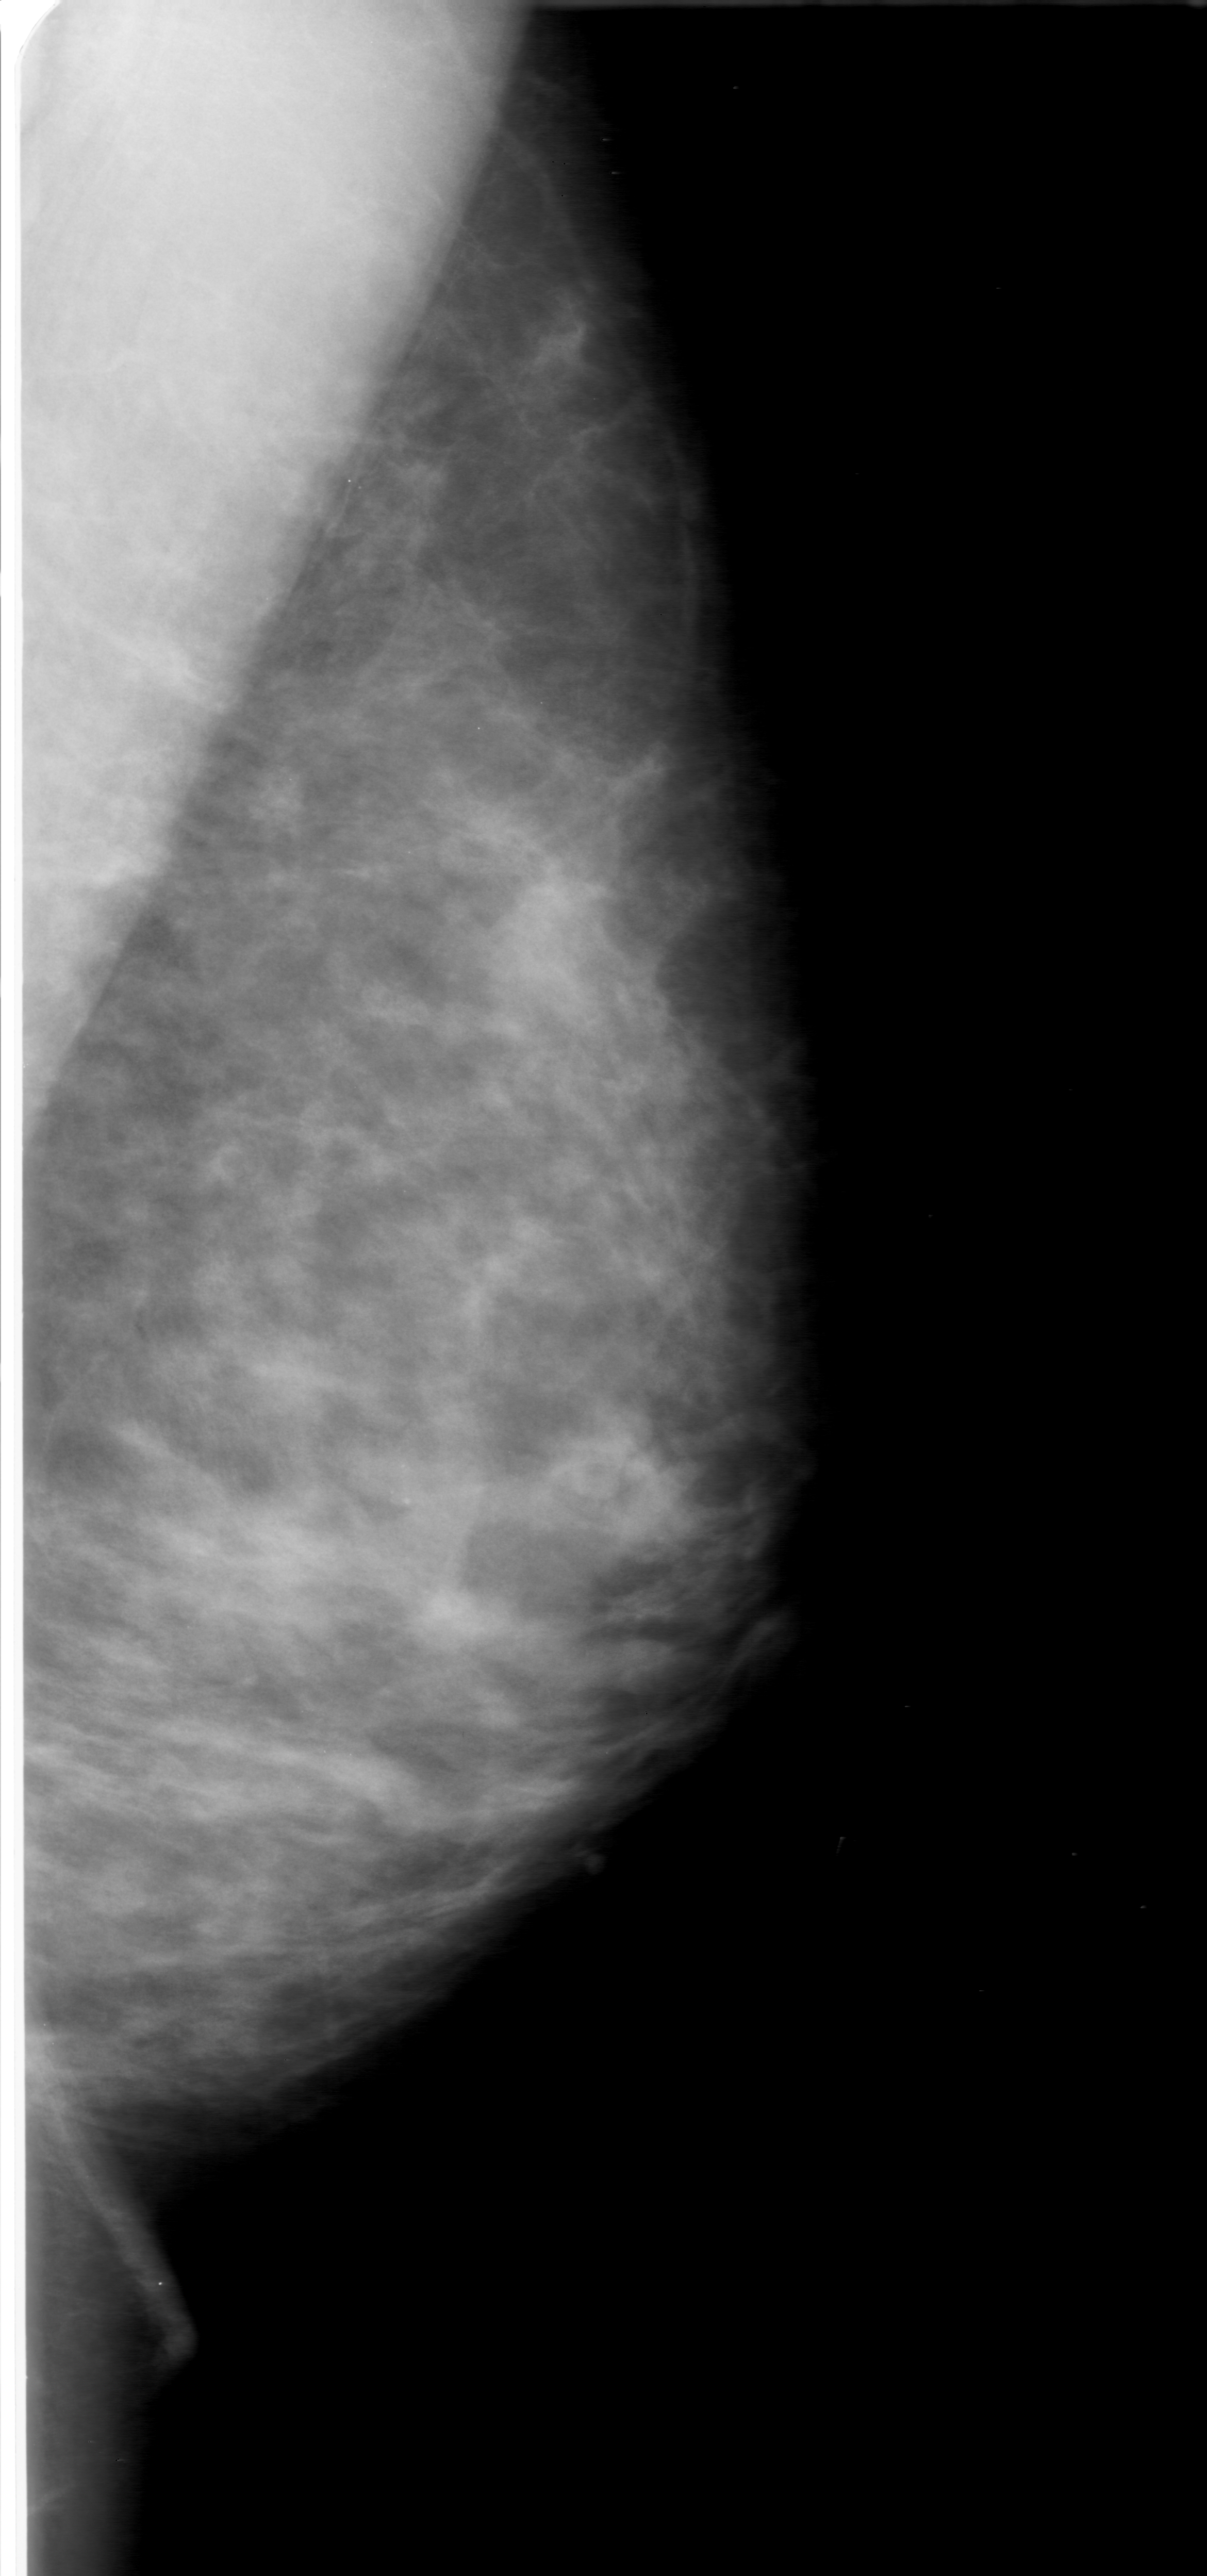
Scanned film-screen mammogram. Left breast. Mediolateral oblique (MLO) view. Breast composition: heterogeneously dense (BI-RADS density category 3 of 4). 1207 × 2576 image matrix.
Expert-marked regions of interest on this film, with their recorded descriptors:
- mass, shape lobulated, margins microlobulated; BI-RADS assessment category 0 (incomplete: needs additional imaging); subtlety rating 3 on a 1 (subtle) to 5 (obvious) scale; pathology result (as recorded, not read from the image): benign: bounding box (x1, y1, x2, y2) in pixels: (540, 1393, 717, 1572)